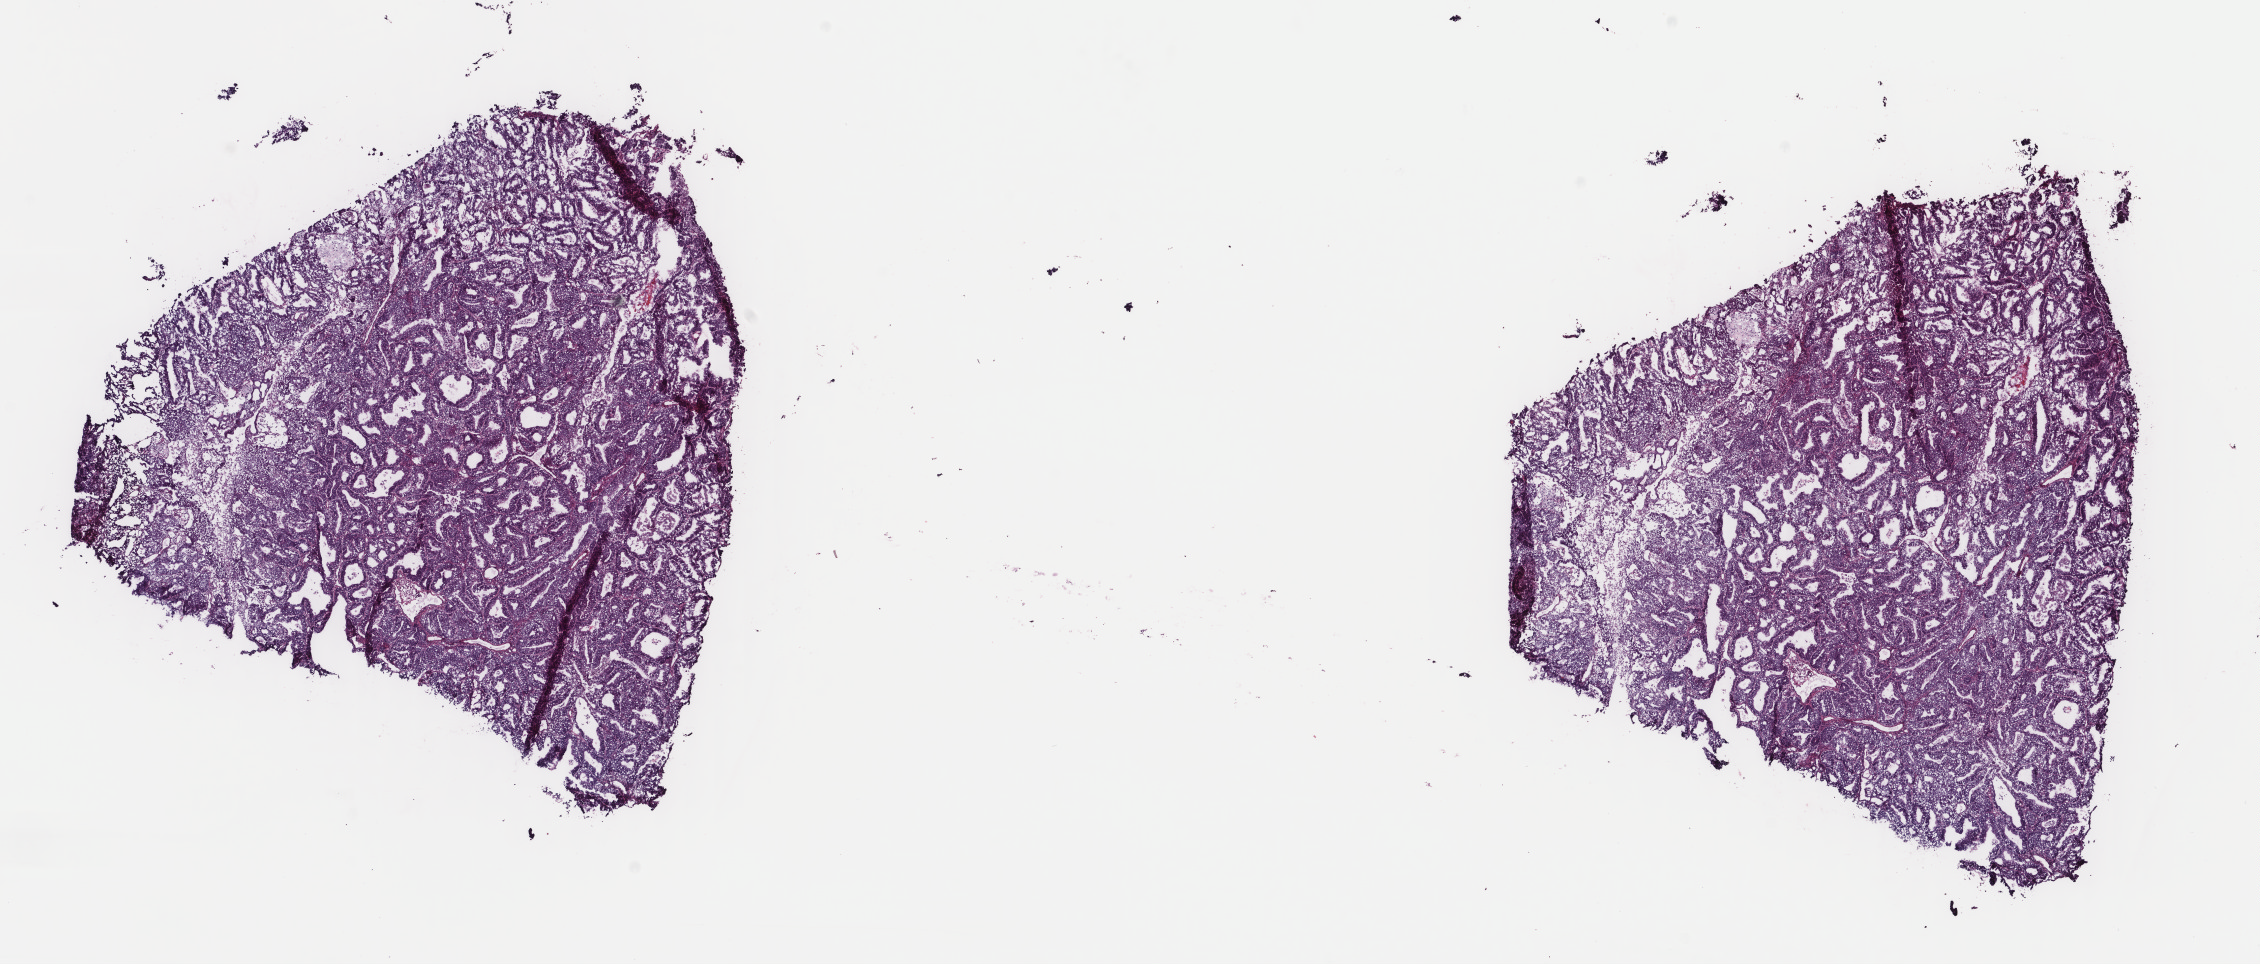
H&E-stained whole-slide image — a low-resolution overview of the entire scanned area, about 17.9 x 7.7 mm, frozen section from the top of the tissue portion, primary tumour sample from the uterus. Patient: female, age at initial diagnosis 54 years. Histologic grade: G2 (moderately differentiated). Slide review estimates, as recorded: tumour cells 70%, tumour nuclei 90%, normal cells 0%, stromal cells 10%, necrosis 20%. Infiltration values recorded for this section: lymphocyte infiltration 30%, monocyte infiltration 0%, neutrophil infiltration 10%.
FIGO stage: II. Pathologic diagnosis: Endometrioid adenocarcinoma, NOS (endometrium). Lymph nodes positive (case pathology): 0 of 19 examined.